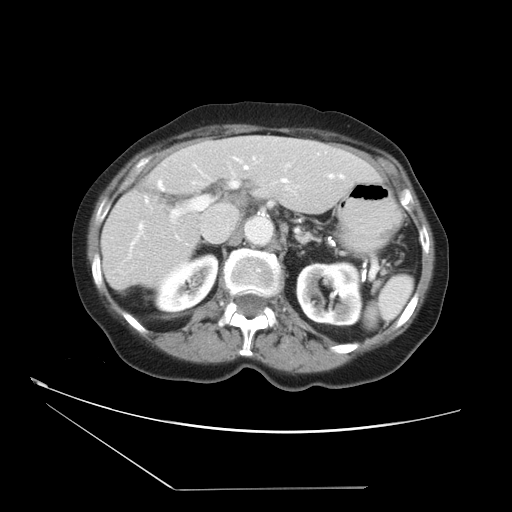
Contrast-enhanced abdominal CT, one axial slice; position 20 of 36 along the scan axis; 120 kVp; intravenous contrast given; soft-tissue window (W 400 / L 40 HU); 5 mm slice thickness; 512 × 512 image matrix, field of view 384 × 384 mm. Female patient, age 81 years. Case-level facts recorded for this patient, not image findings: diagnosis: colorectal cancer liver metastases, imaged before liver resection; multiple liver metastases: no; largest metastasis: 1.6 cm.
Annotated regions visible in this slice (expert manual segmentation):
- hepatic veins: bounding box [x1, y1, x2, y2] px = [130, 167, 333, 251]
- liver: [102, 137, 382, 291]
- planned liver remnant (the part of the liver to remain after resection): [101, 139, 382, 291]
- portal vein (with intrahepatic branches): [145, 182, 237, 224]